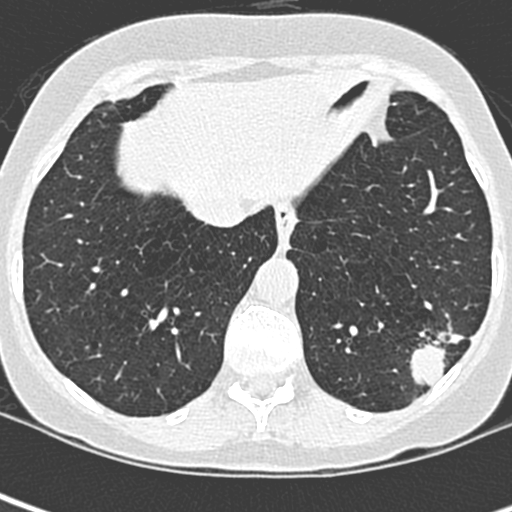
Low-dose screening chest CT, one axial slice; position 72 of 252 along the scan axis; 120 kVp; lung window (W 1500 / L -600 HU); 1.3 mm slice thickness; 512 × 512 image matrix, field of view 271 × 271 mm.
Outlined on this slice (outlined manually by an expert reader):
- lesion 1 (tumor, lower lobe of left lung): bounding box [x1, y1, x2, y2] px = [410, 326, 465, 387]